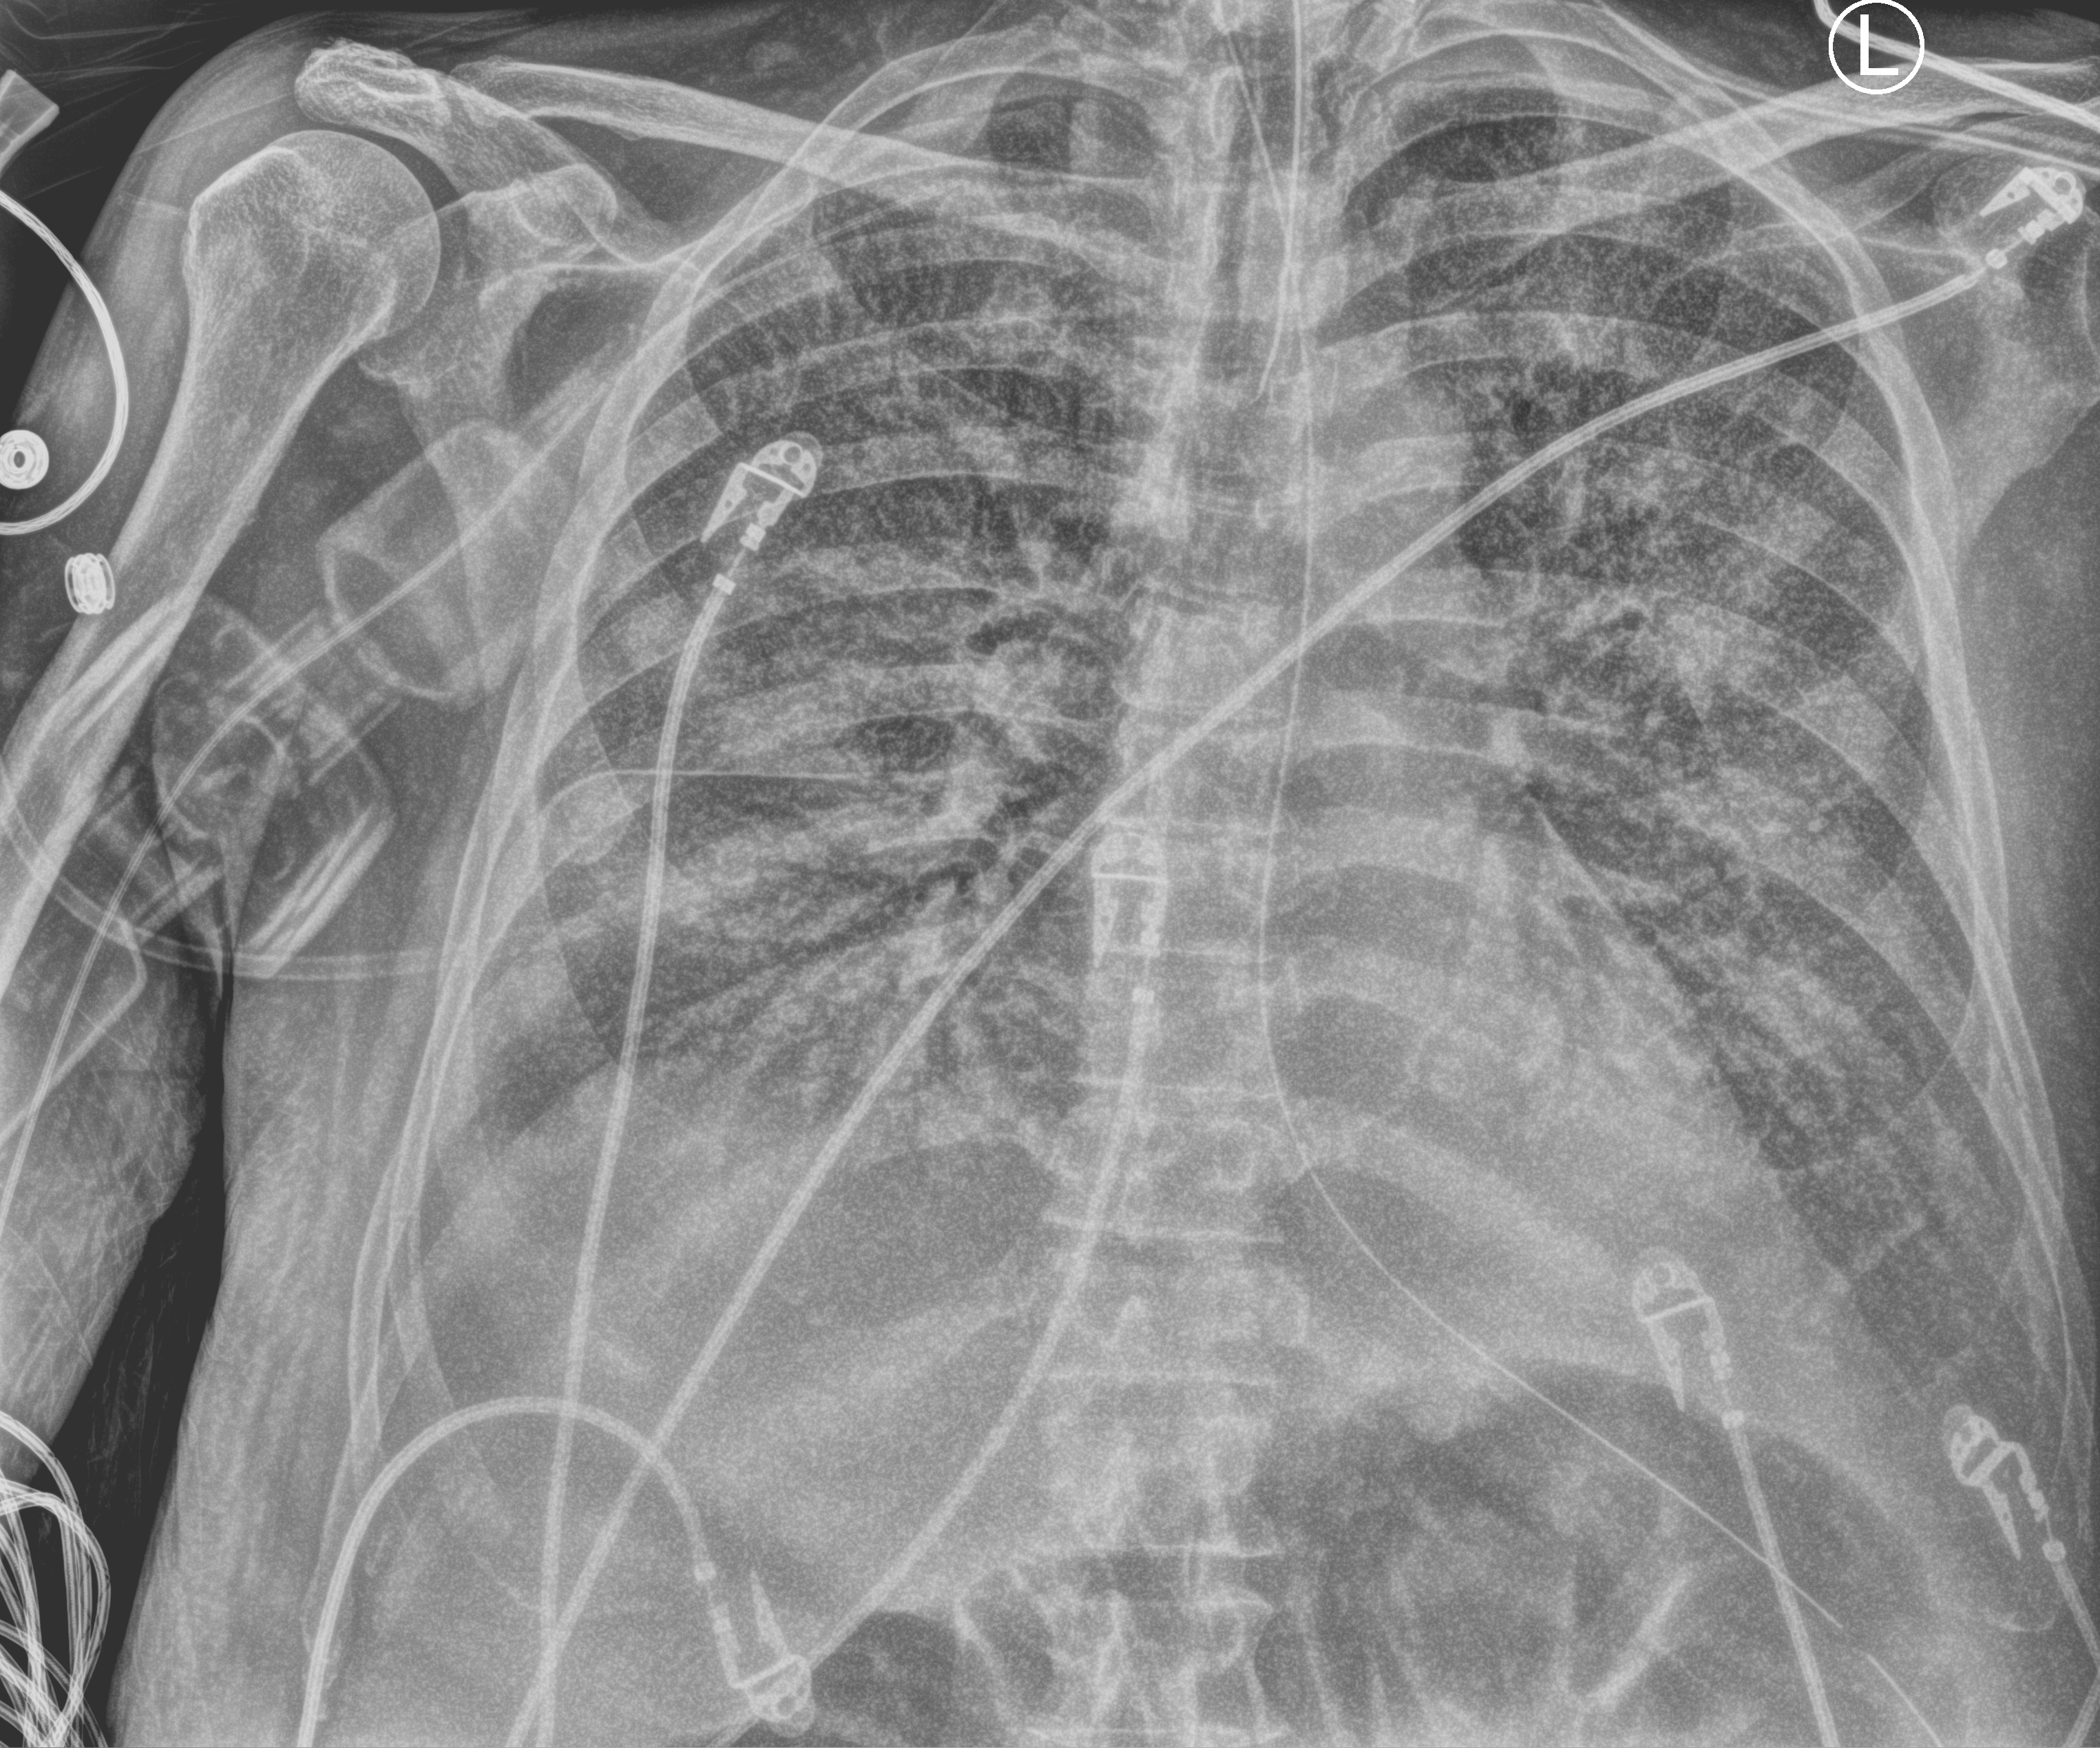
Chest X-ray (portable), anteroposterior (AP) projection. Patient hospitalised with COVID-19; male, aged 60–74 years.
Hospital-stay facts (about this admission, not read from this image; timing relative to this image not recorded): other chronic lung disease (admission record): no.